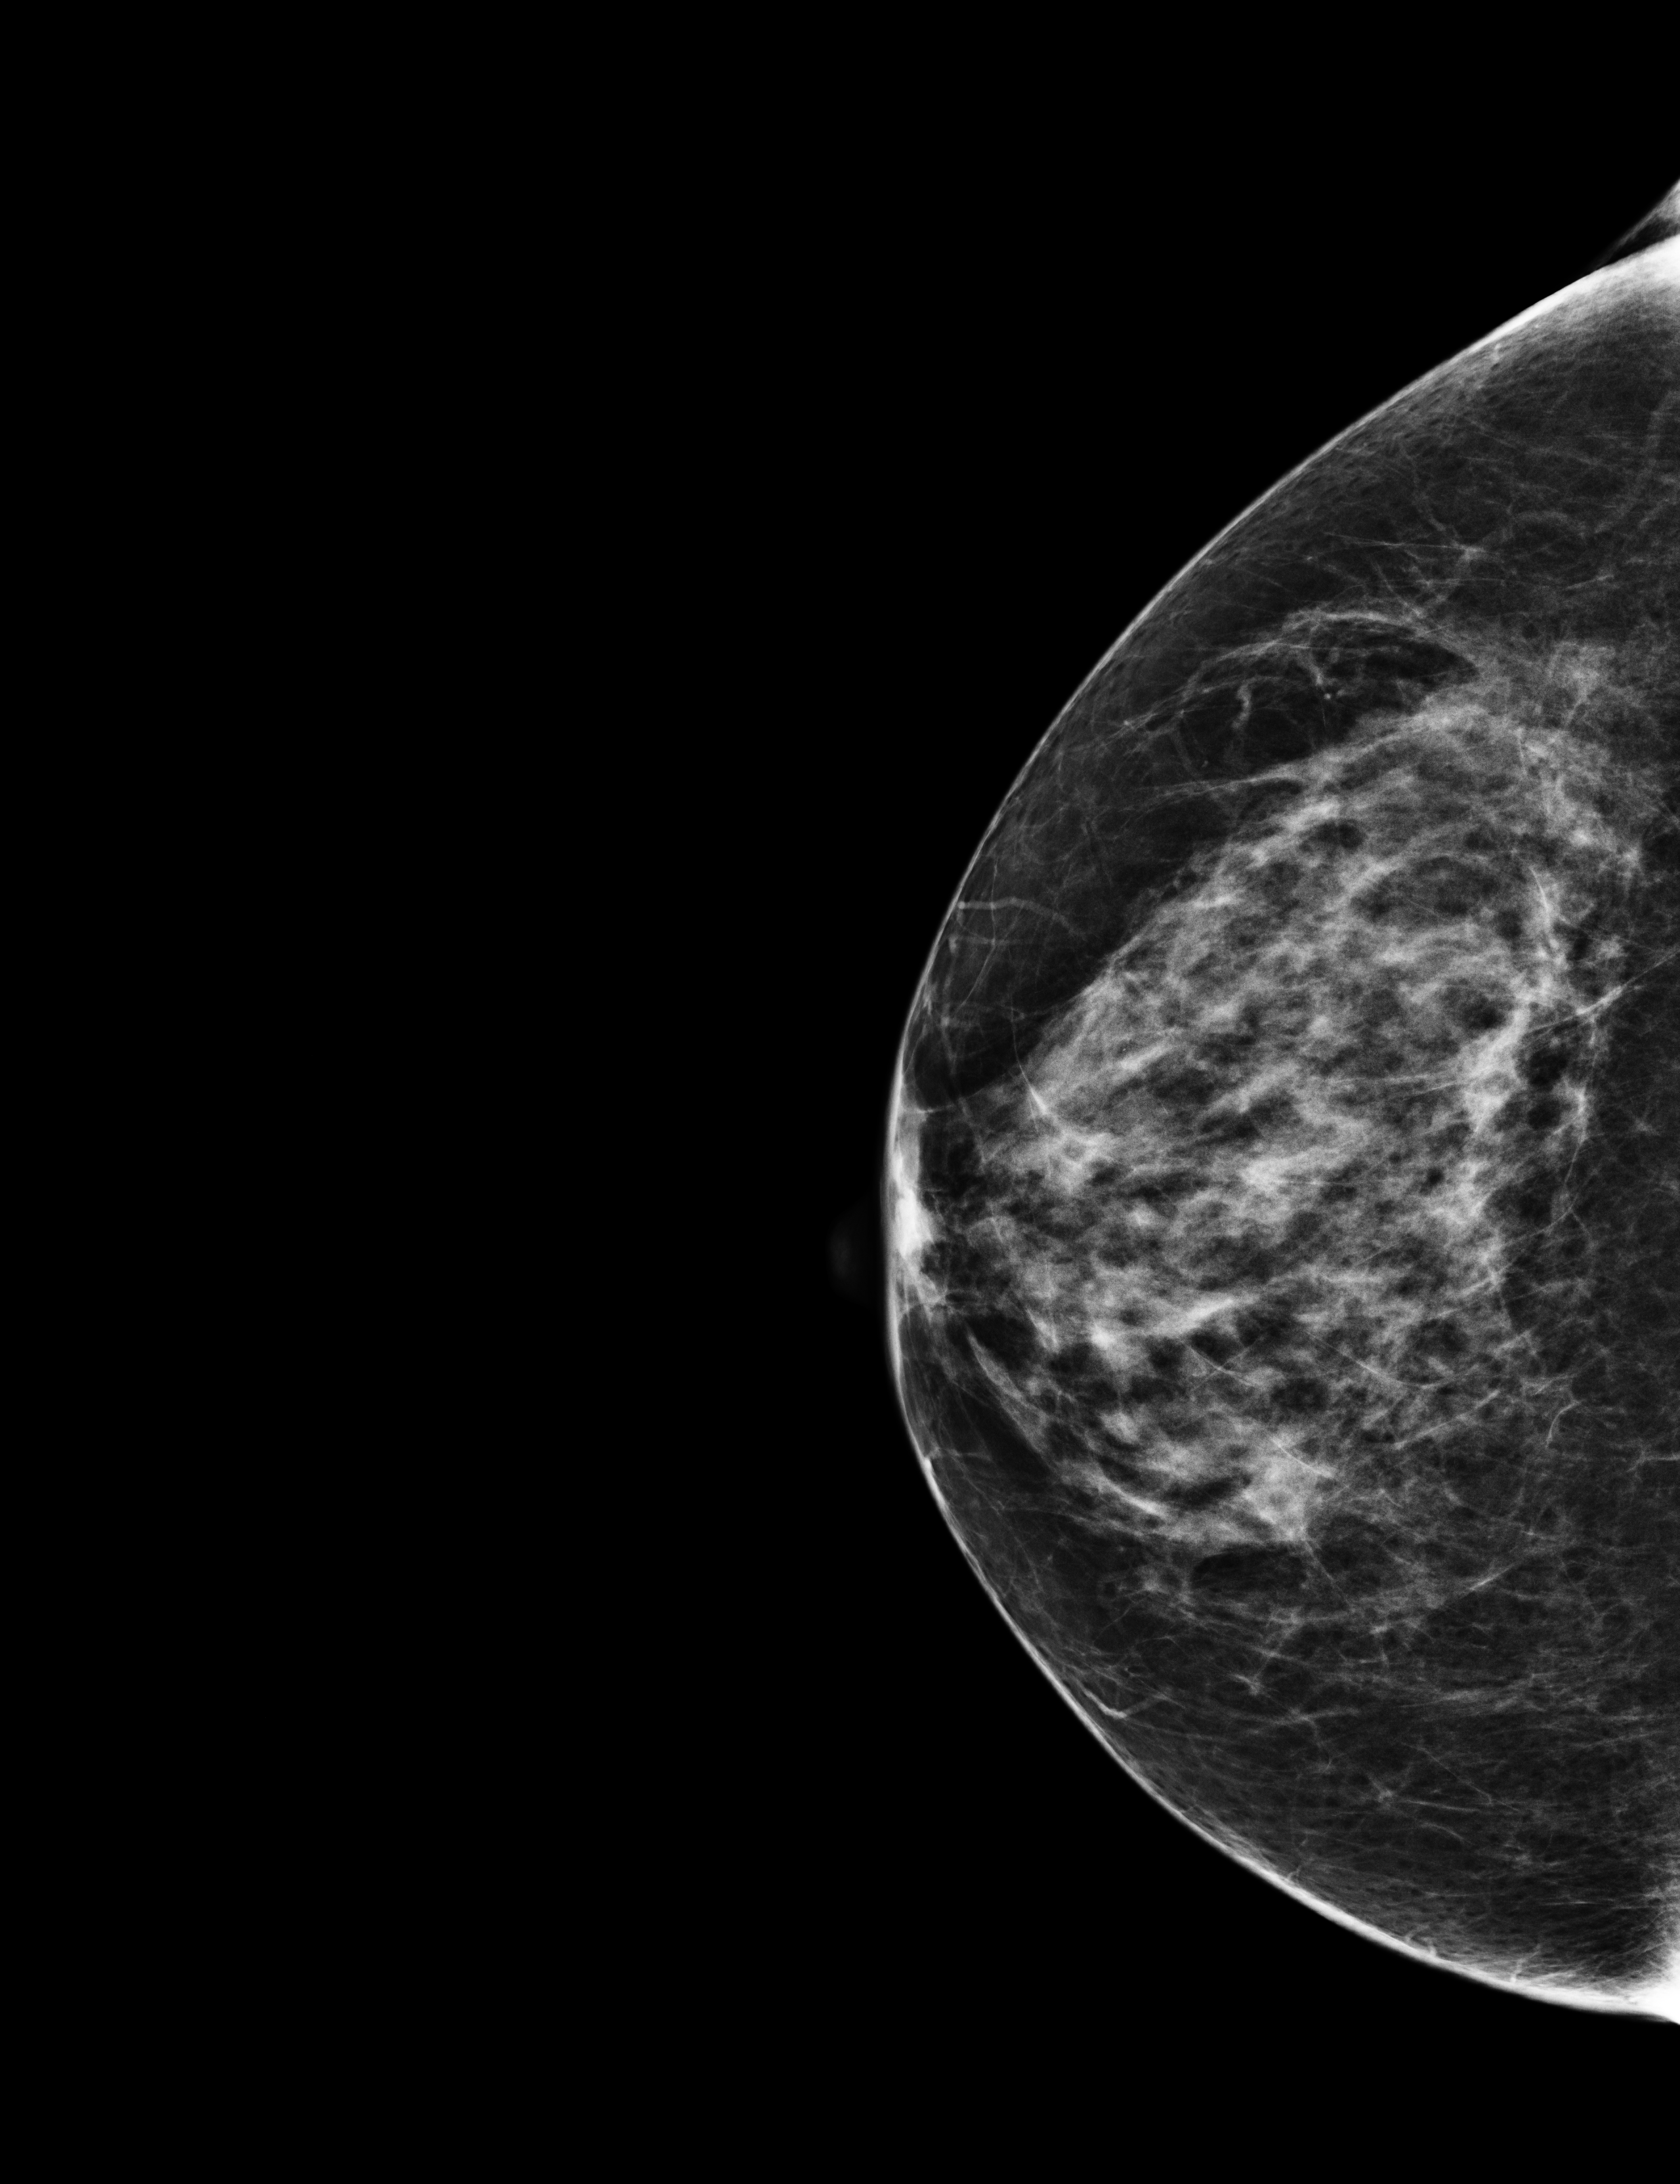
Annual screening mammography examination, compressed breast thickness 56 mm. Female patient, age 59 years.
Image type: full-field digital mammogram. Breast: right. Projection: cranio-caudal projection.